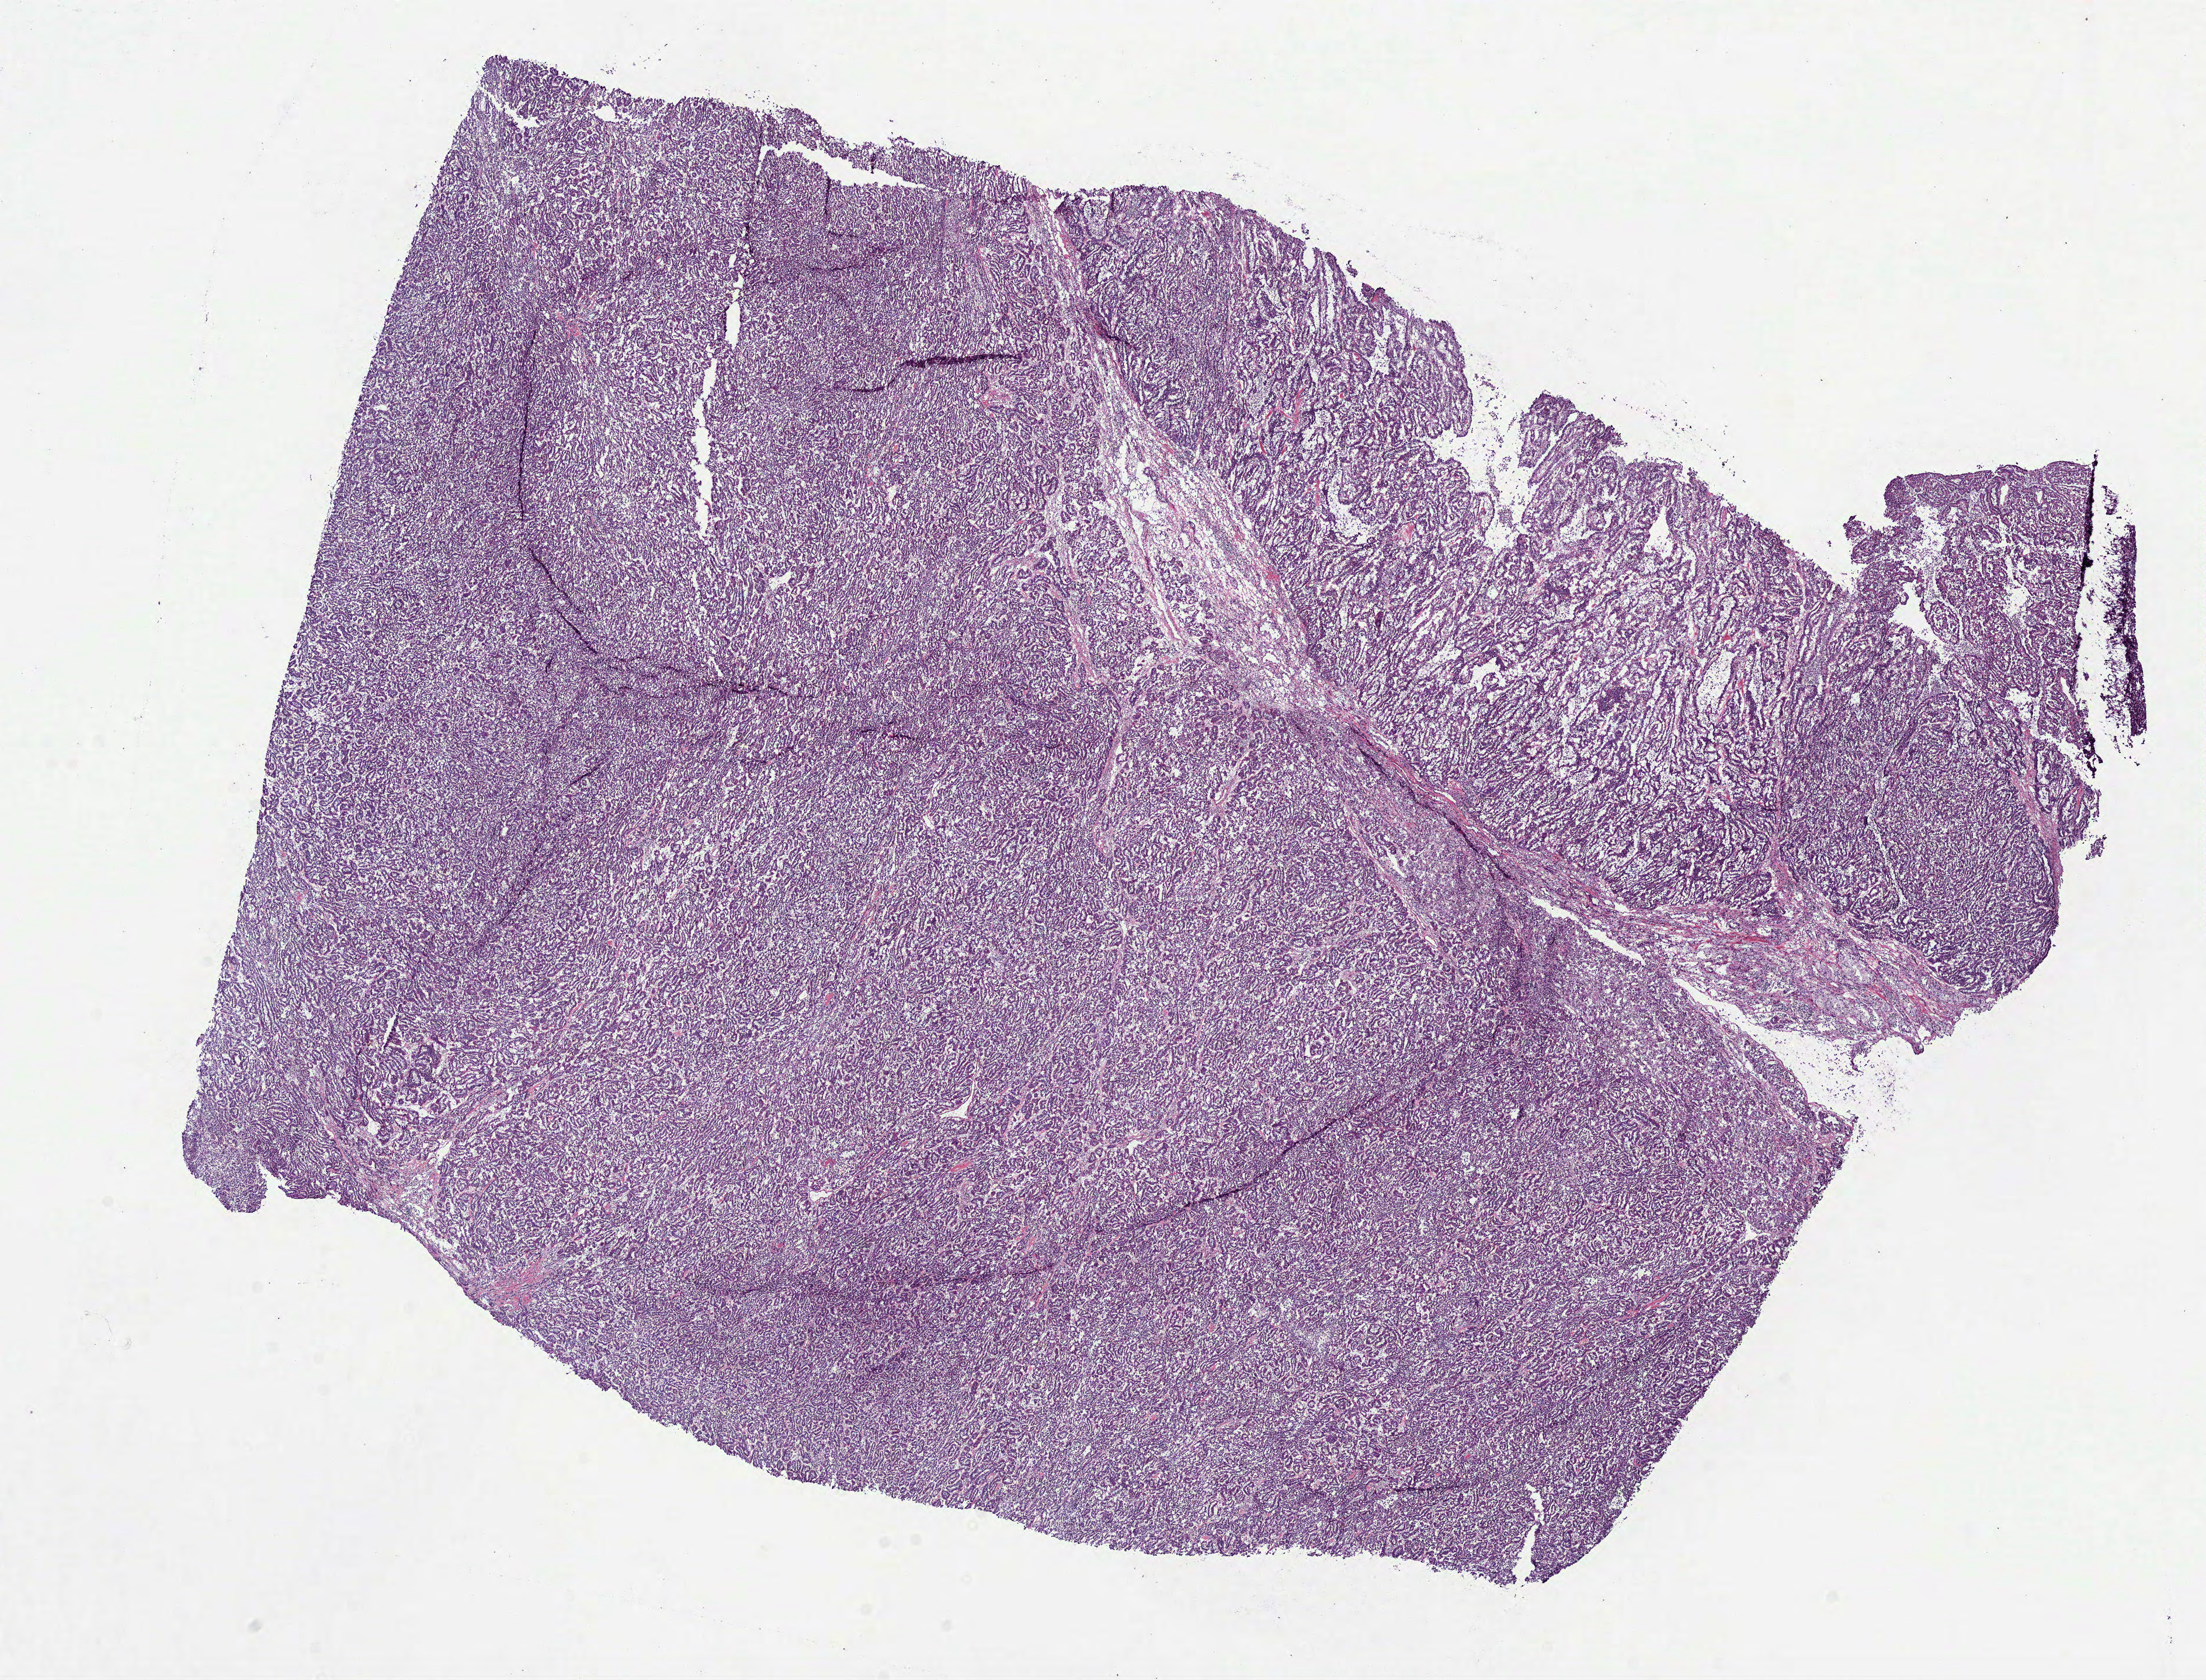
H&E whole-slide image, shown as a low-resolution overview of the whole scanned area (about 15.2 x 11.6 mm, acquisition: 40x scan), frozen section from the bottom of the tissue portion, primary tumour sample from the kidney. Patient: male, age at initial diagnosis 63 years. Pathologist review of this section (percent, as recorded): tumour cells 95%, tumour nuclei 85%, normal cells 0%, stromal cells 5%, necrosis 0%.
- AJCC pathologic stage: III
- lymph nodes positive (case pathology): 0 of 15 examined
- pathologic diagnosis: Papillary adenocarcinoma, NOS